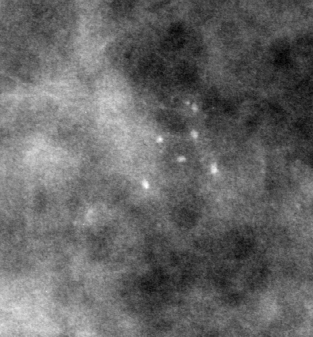
Cropped region of a digitized screen-film mammogram centred on a radiologist-marked abnormality; left breast; MLO view.
- Finding: calcifications, morphology punctate, distribution clustered; BI-RADS assessment category 5; subtlety rating 5 on a 1 (subtle) to 5 (obvious) scale; pathology (as recorded): malignant.